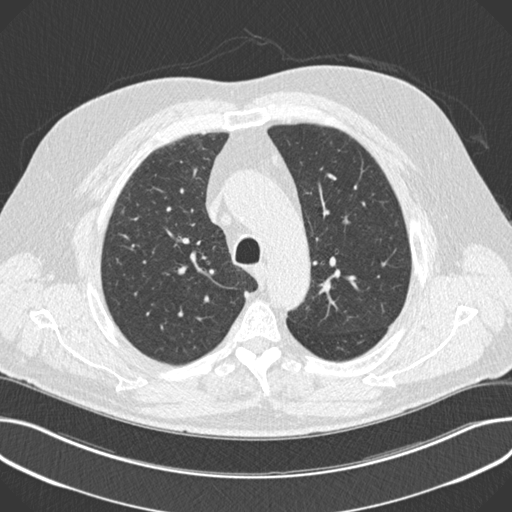
Low-dose screening chest CT, axial slice, baseline screening round, lung window (W 1500 / L -600 HU), 2 mm slice thickness, standard (soft-tissue) reconstruction kernel (B30f), slice 49 of 202 in the series. Male participant, aged 64 years at enrolment. Current smoker at enrolment.
Expert reader's lesion annotation, bounding box (x1, y1, x2, y2) in pixels: (109, 199, 134, 224). No non-calcified nodule or mass ≥4 mm was recorded by the screening reader at this exam. Participant outcome: lung cancer diagnosed 854 days after this screen (after the third annual screen) — squamous cell carcinoma, NOS, right upper lobe, moderately differentiated (G2), stage IA (AJCC 6th edition), 7 mm at pathology.